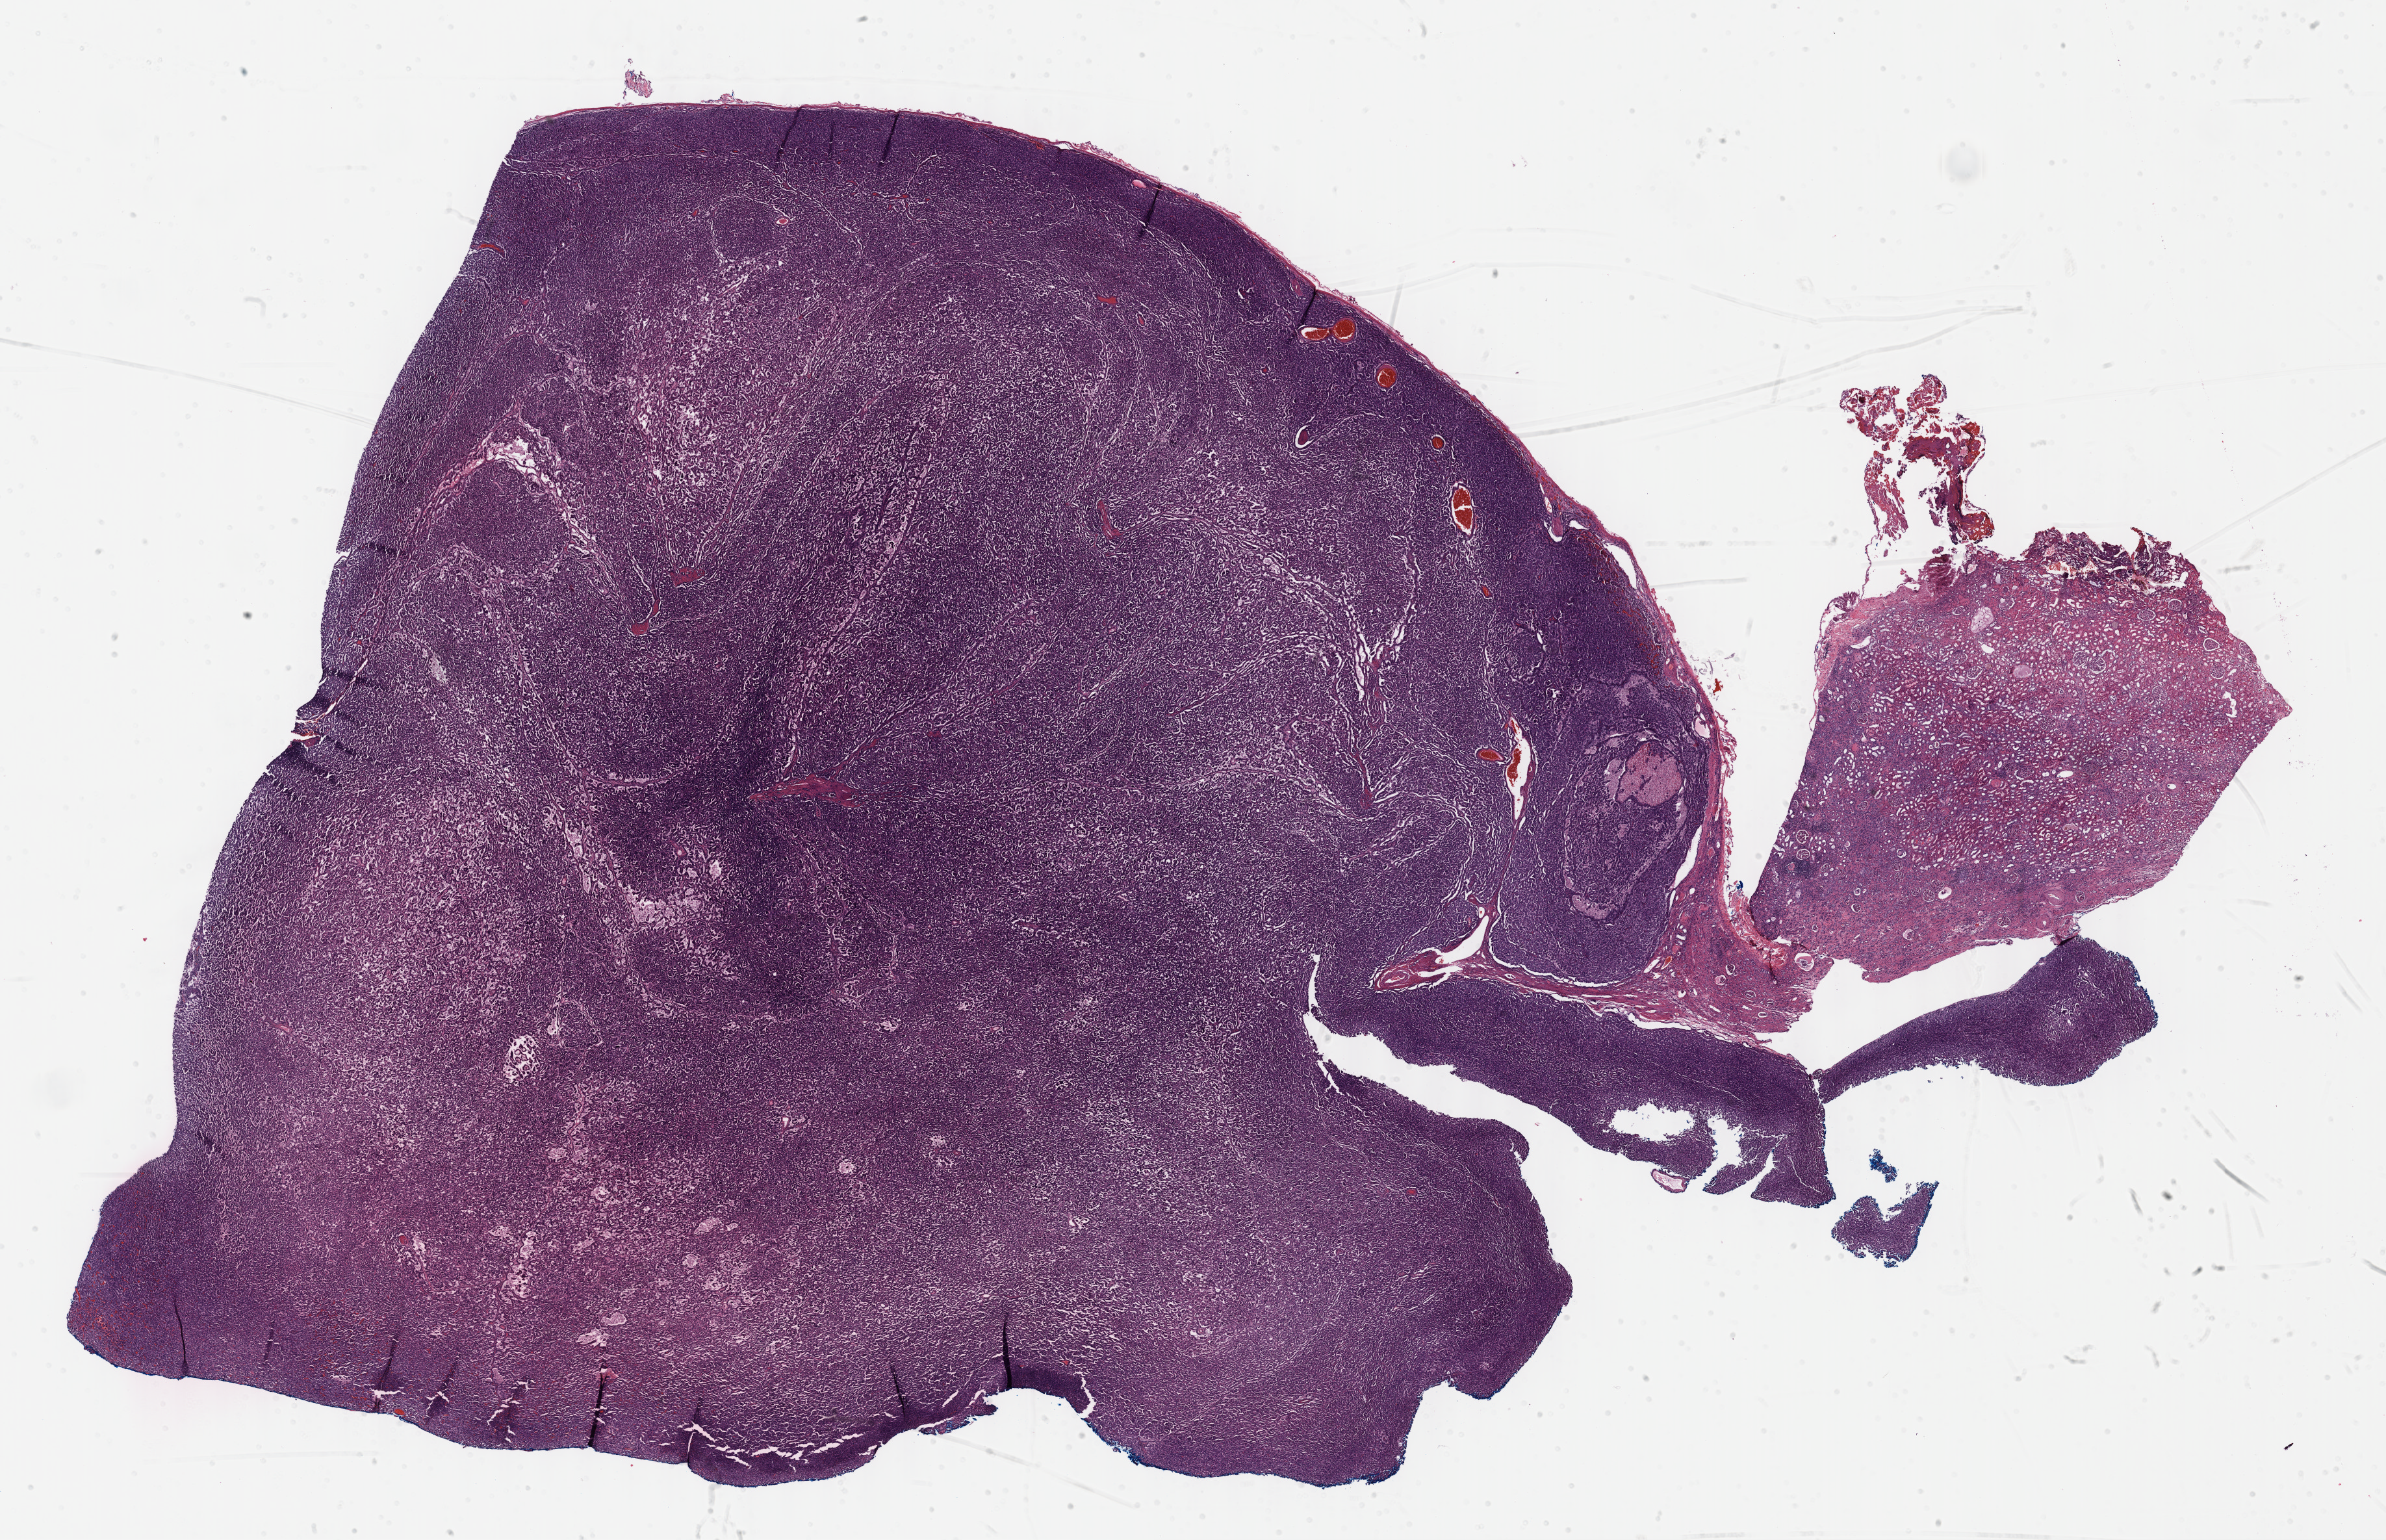
Digitized H&E tissue section (whole slide), a low-resolution overview of the entire scanned area, about 29.7 x 19.2 mm (slide scanned at 40x), formalin-fixed paraffin-embedded (FFPE) diagnostic section, kidney, primary tumour sample. Female patient; age at initial diagnosis 66 years.
Pathologic diagnosis: Papillary adenocarcinoma, NOS.